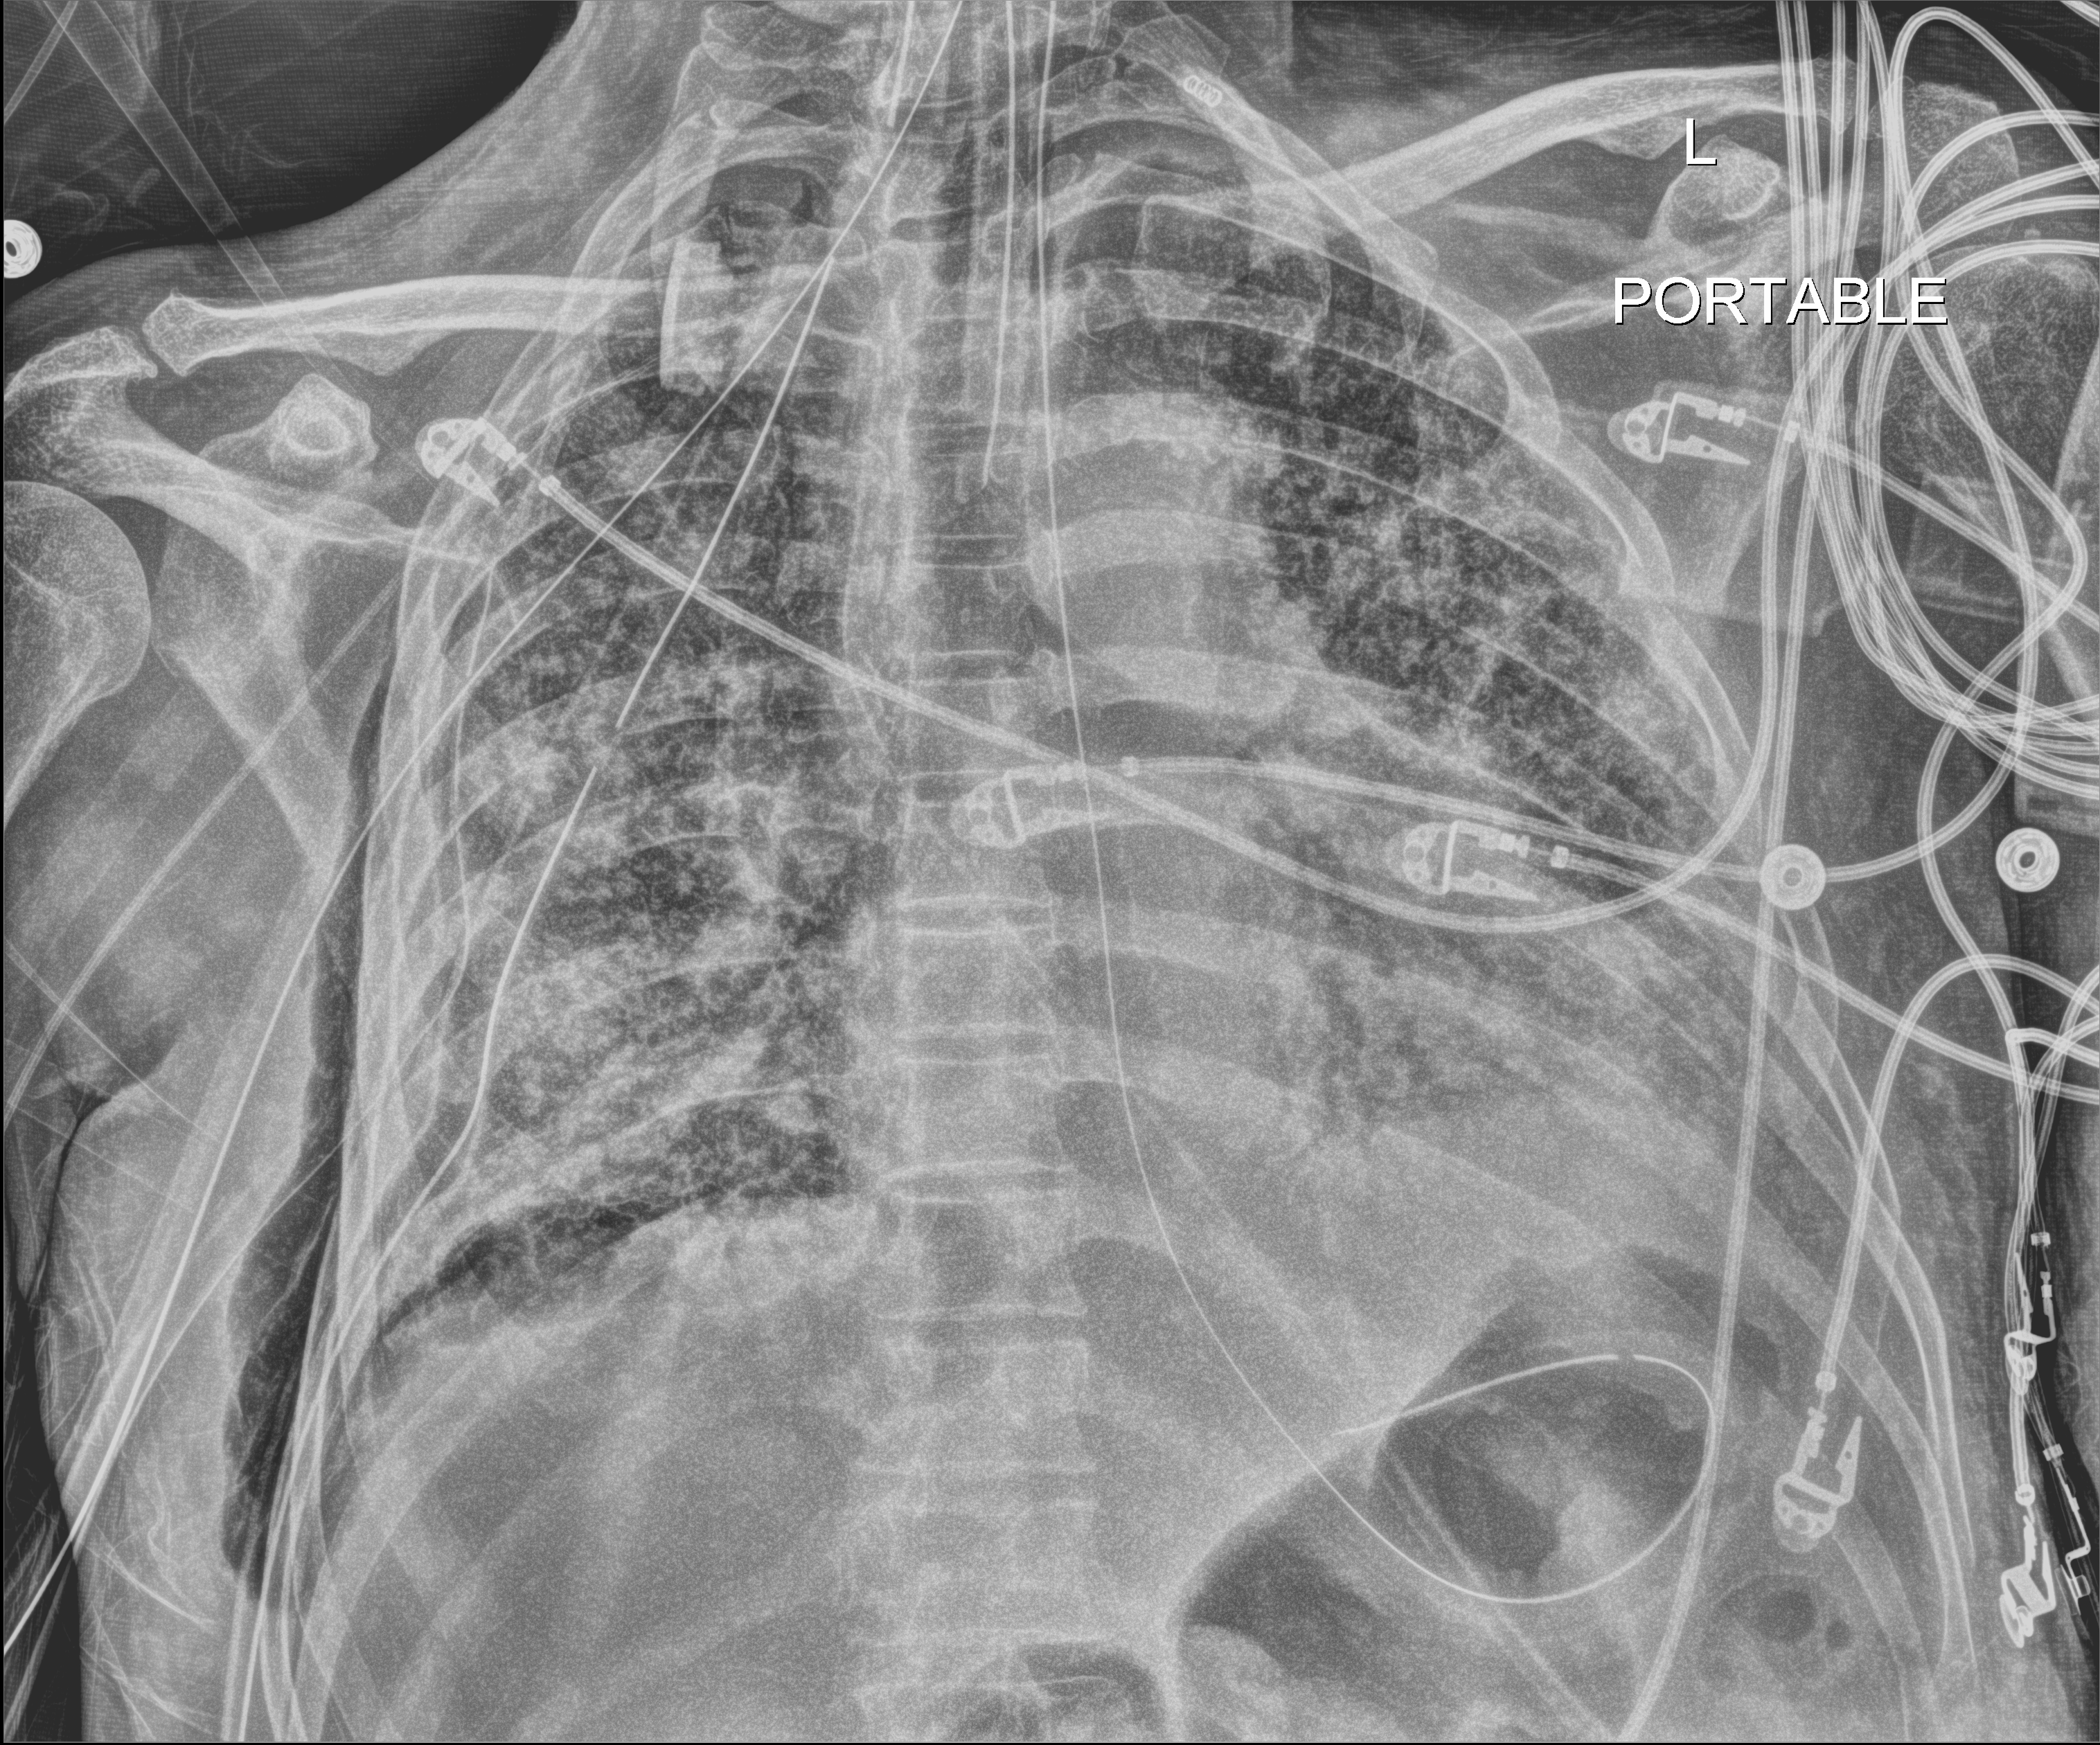
Bedside chest radiograph (digital radiography), anteroposterior (AP) projection. Patient hospitalised with COVID-19; male, aged 60–74 years.
Hospital-stay facts (about this admission, not read from this image; timing relative to this image not recorded):
- length of hospital stay: 37 days
- other chronic lung disease (admission record): no